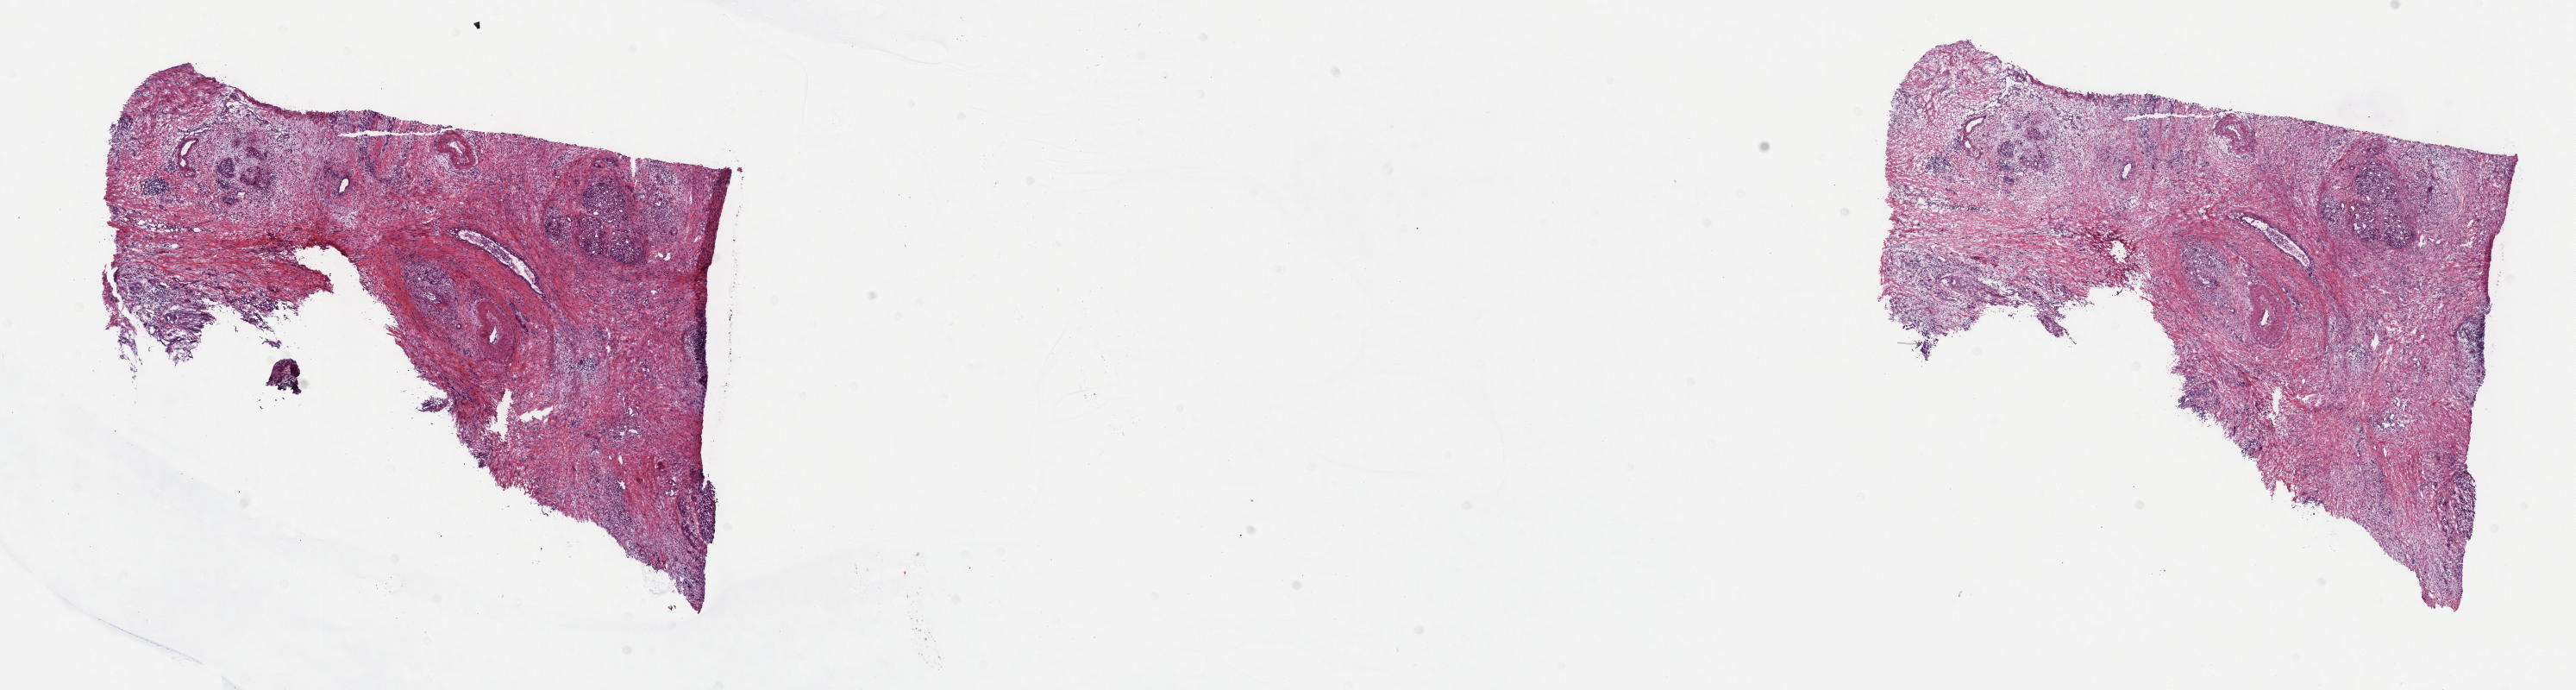
Hematoxylin and eosin (H&E) stained whole-slide image — a low-resolution overview of the entire scanned area, about 24.2 x 6.5 mm (from a 40x scan). Frozen section. Pancreas, primary tumour sample. Patient: female, age at initial diagnosis 50 years. Pathologist review of this section (percent, as recorded): tumour cells 60%, tumour nuclei 60%.
Histologic diagnosis: Infiltrating duct carcinoma, NOS (head of pancreas).